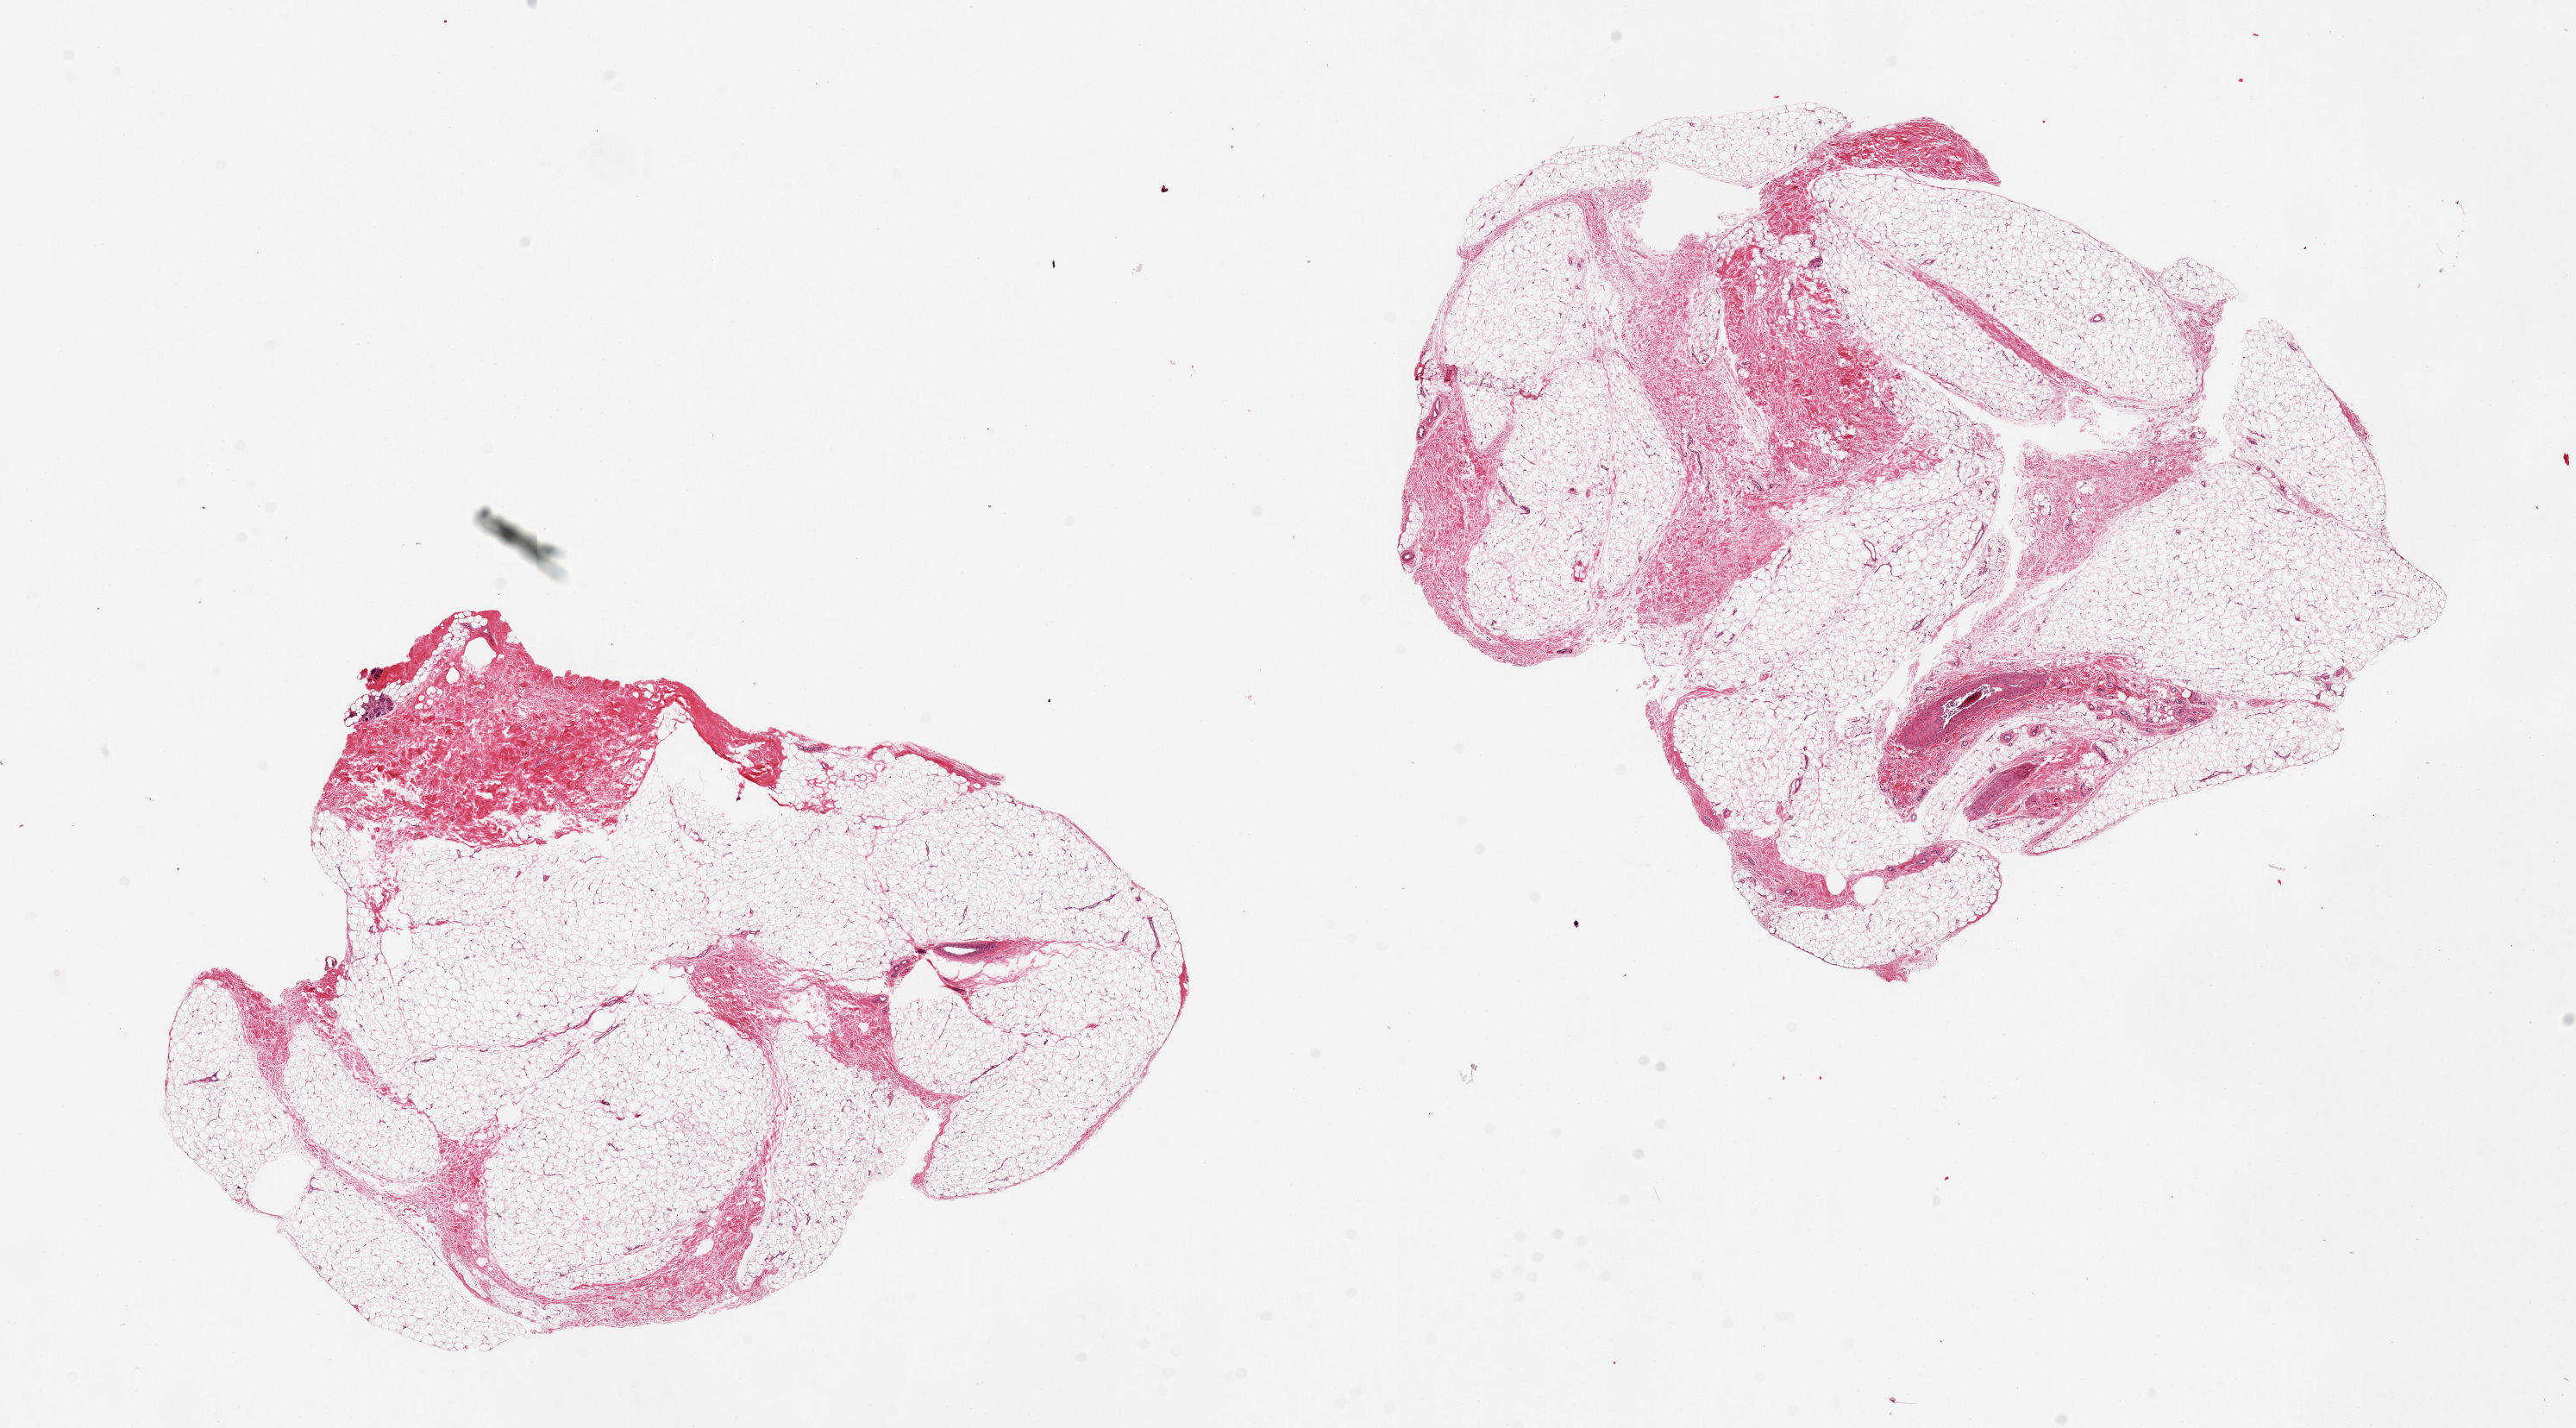
Digitized H&E-stained section — shown as a low-resolution overview of the whole scanned area (about 23.6 x 13.1 mm); PAXgene-fixed paraffin-embedded (PFPE) section; target tissue: adipose tissue; tissue donor sample.
Reviewer comment on this tissue sample: 2 pieces; 20-30% fibrous tissue admixed.